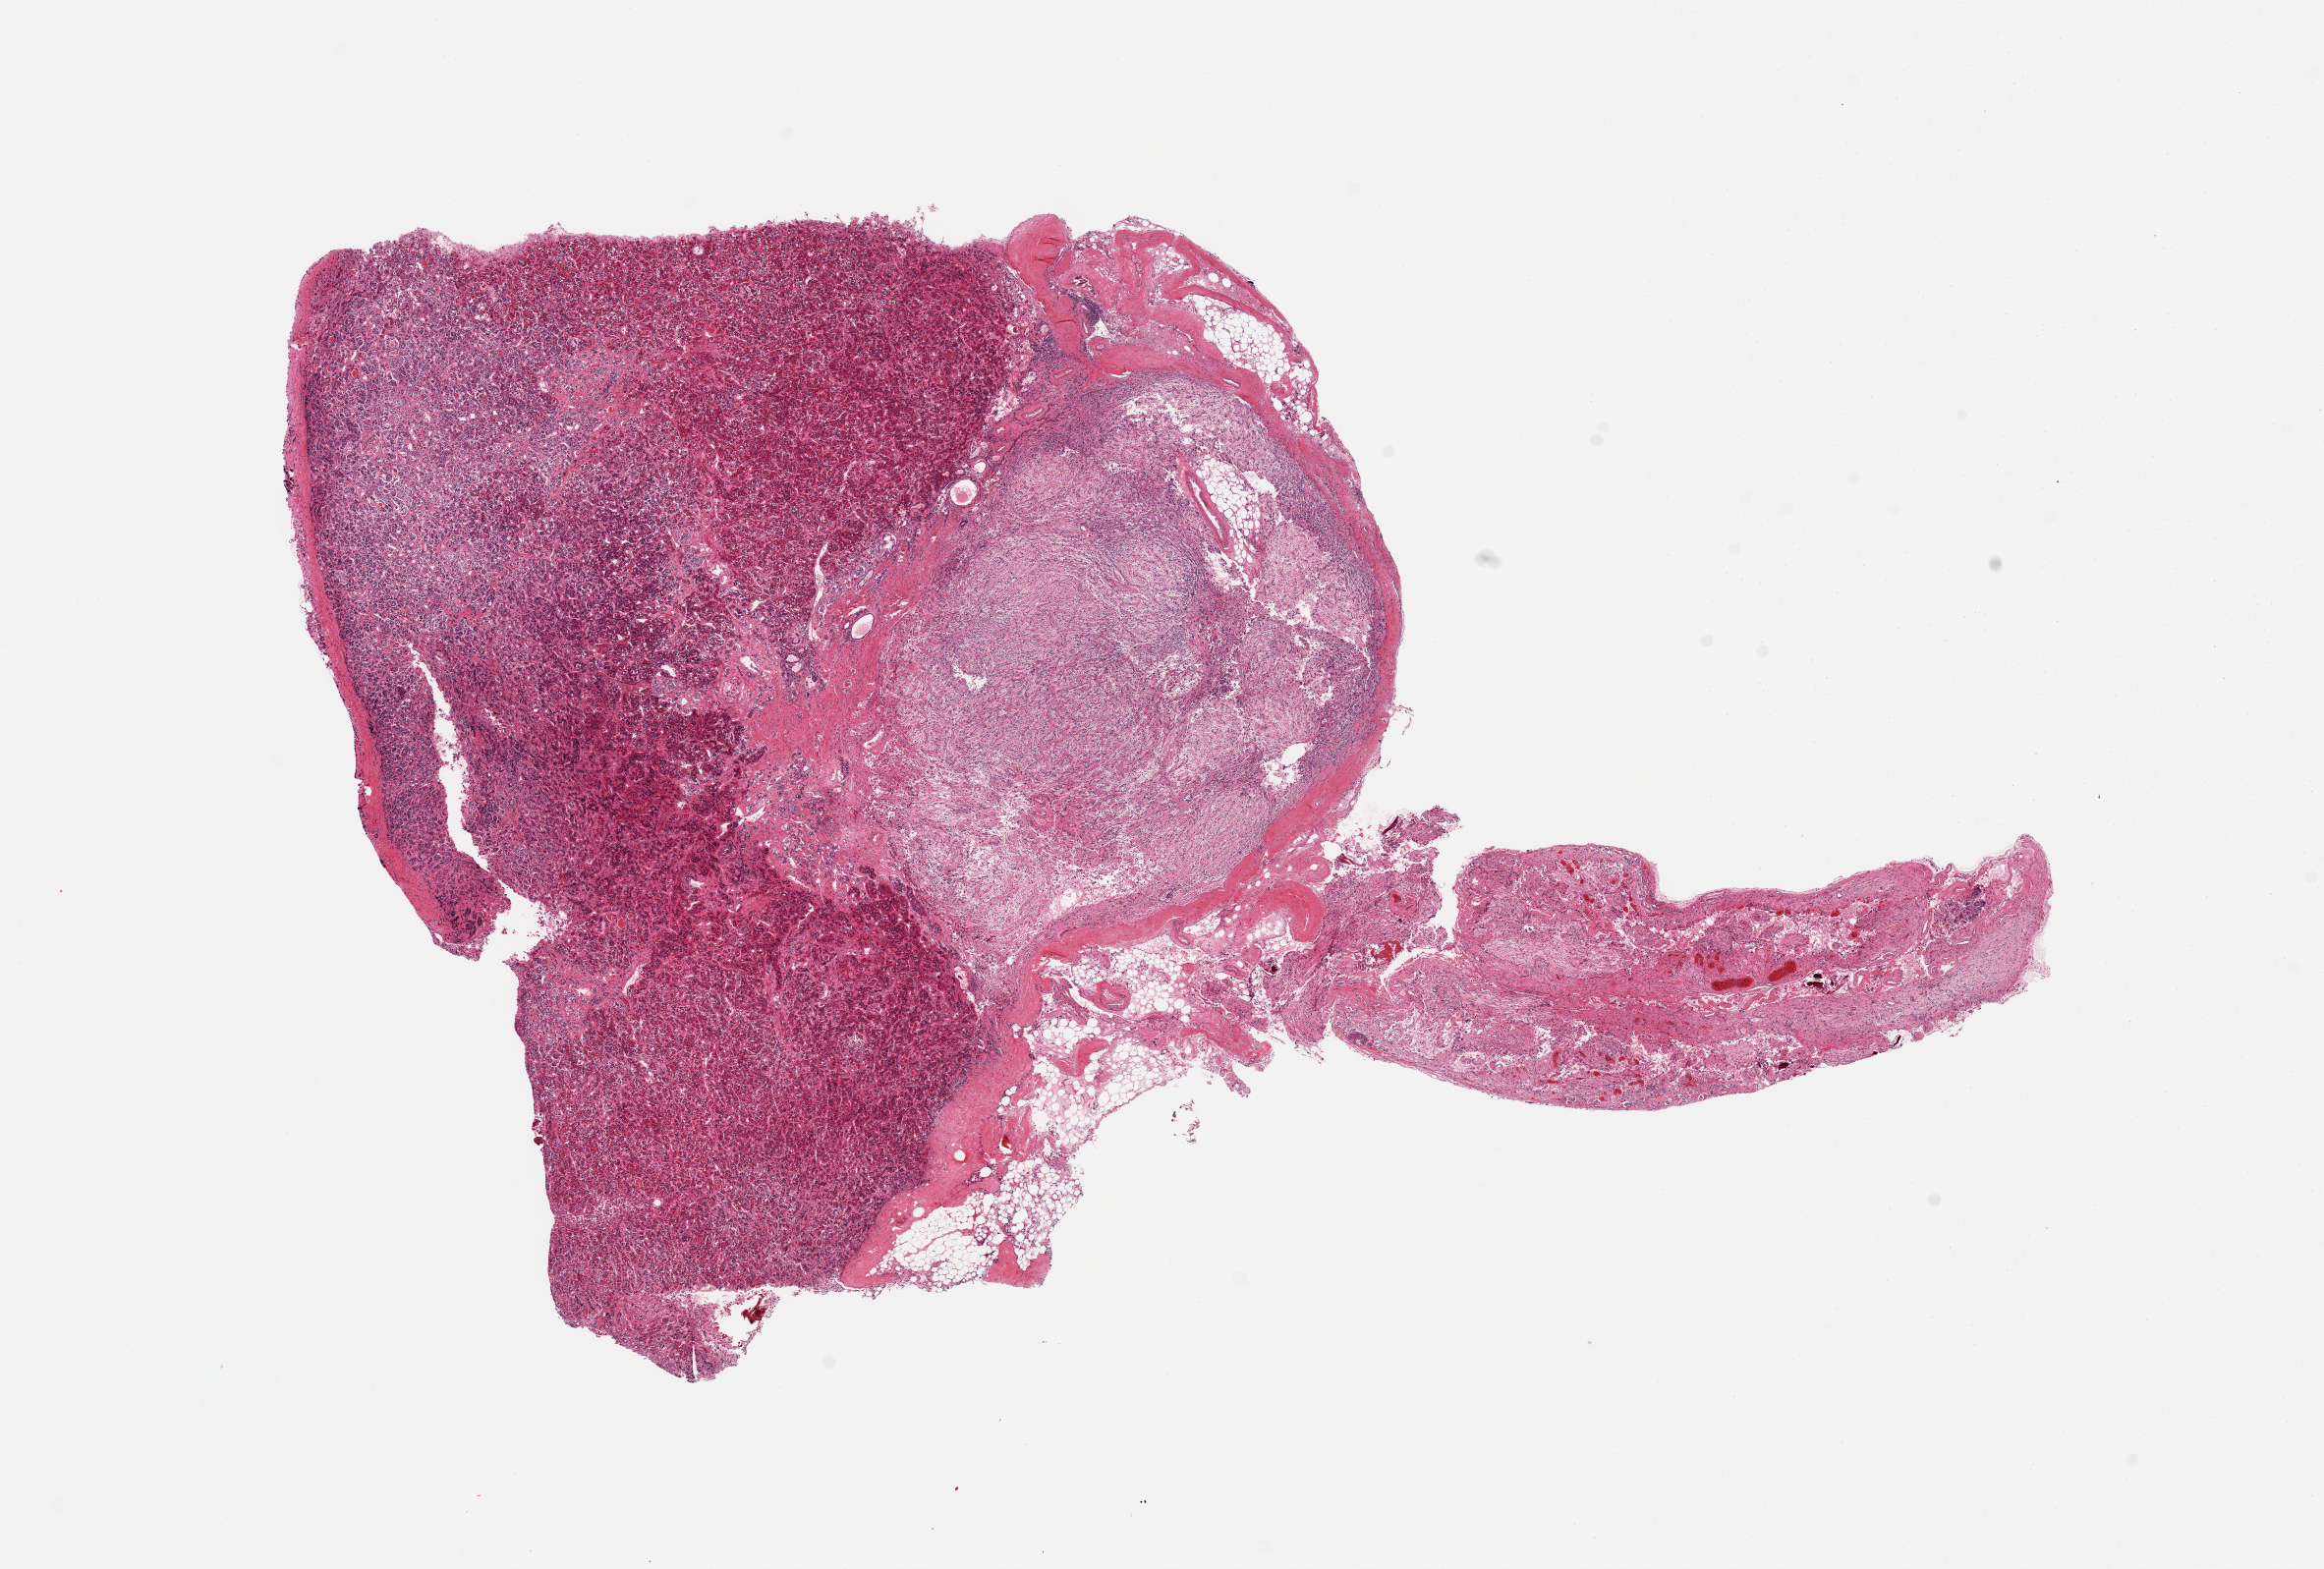
Whole-slide image, H&E stain, brightfield, a low-resolution overview of the entire scanned area, about 18.7 x 12.6 mm. PAXgene-fixed paraffin-embedded (PFPE) section. Section of pituitary (target tissue). Tissue donor sample. Donor: male.
Pathologist's review note for this sample: 1 piece; adenohypophysis, neurohypophysis.